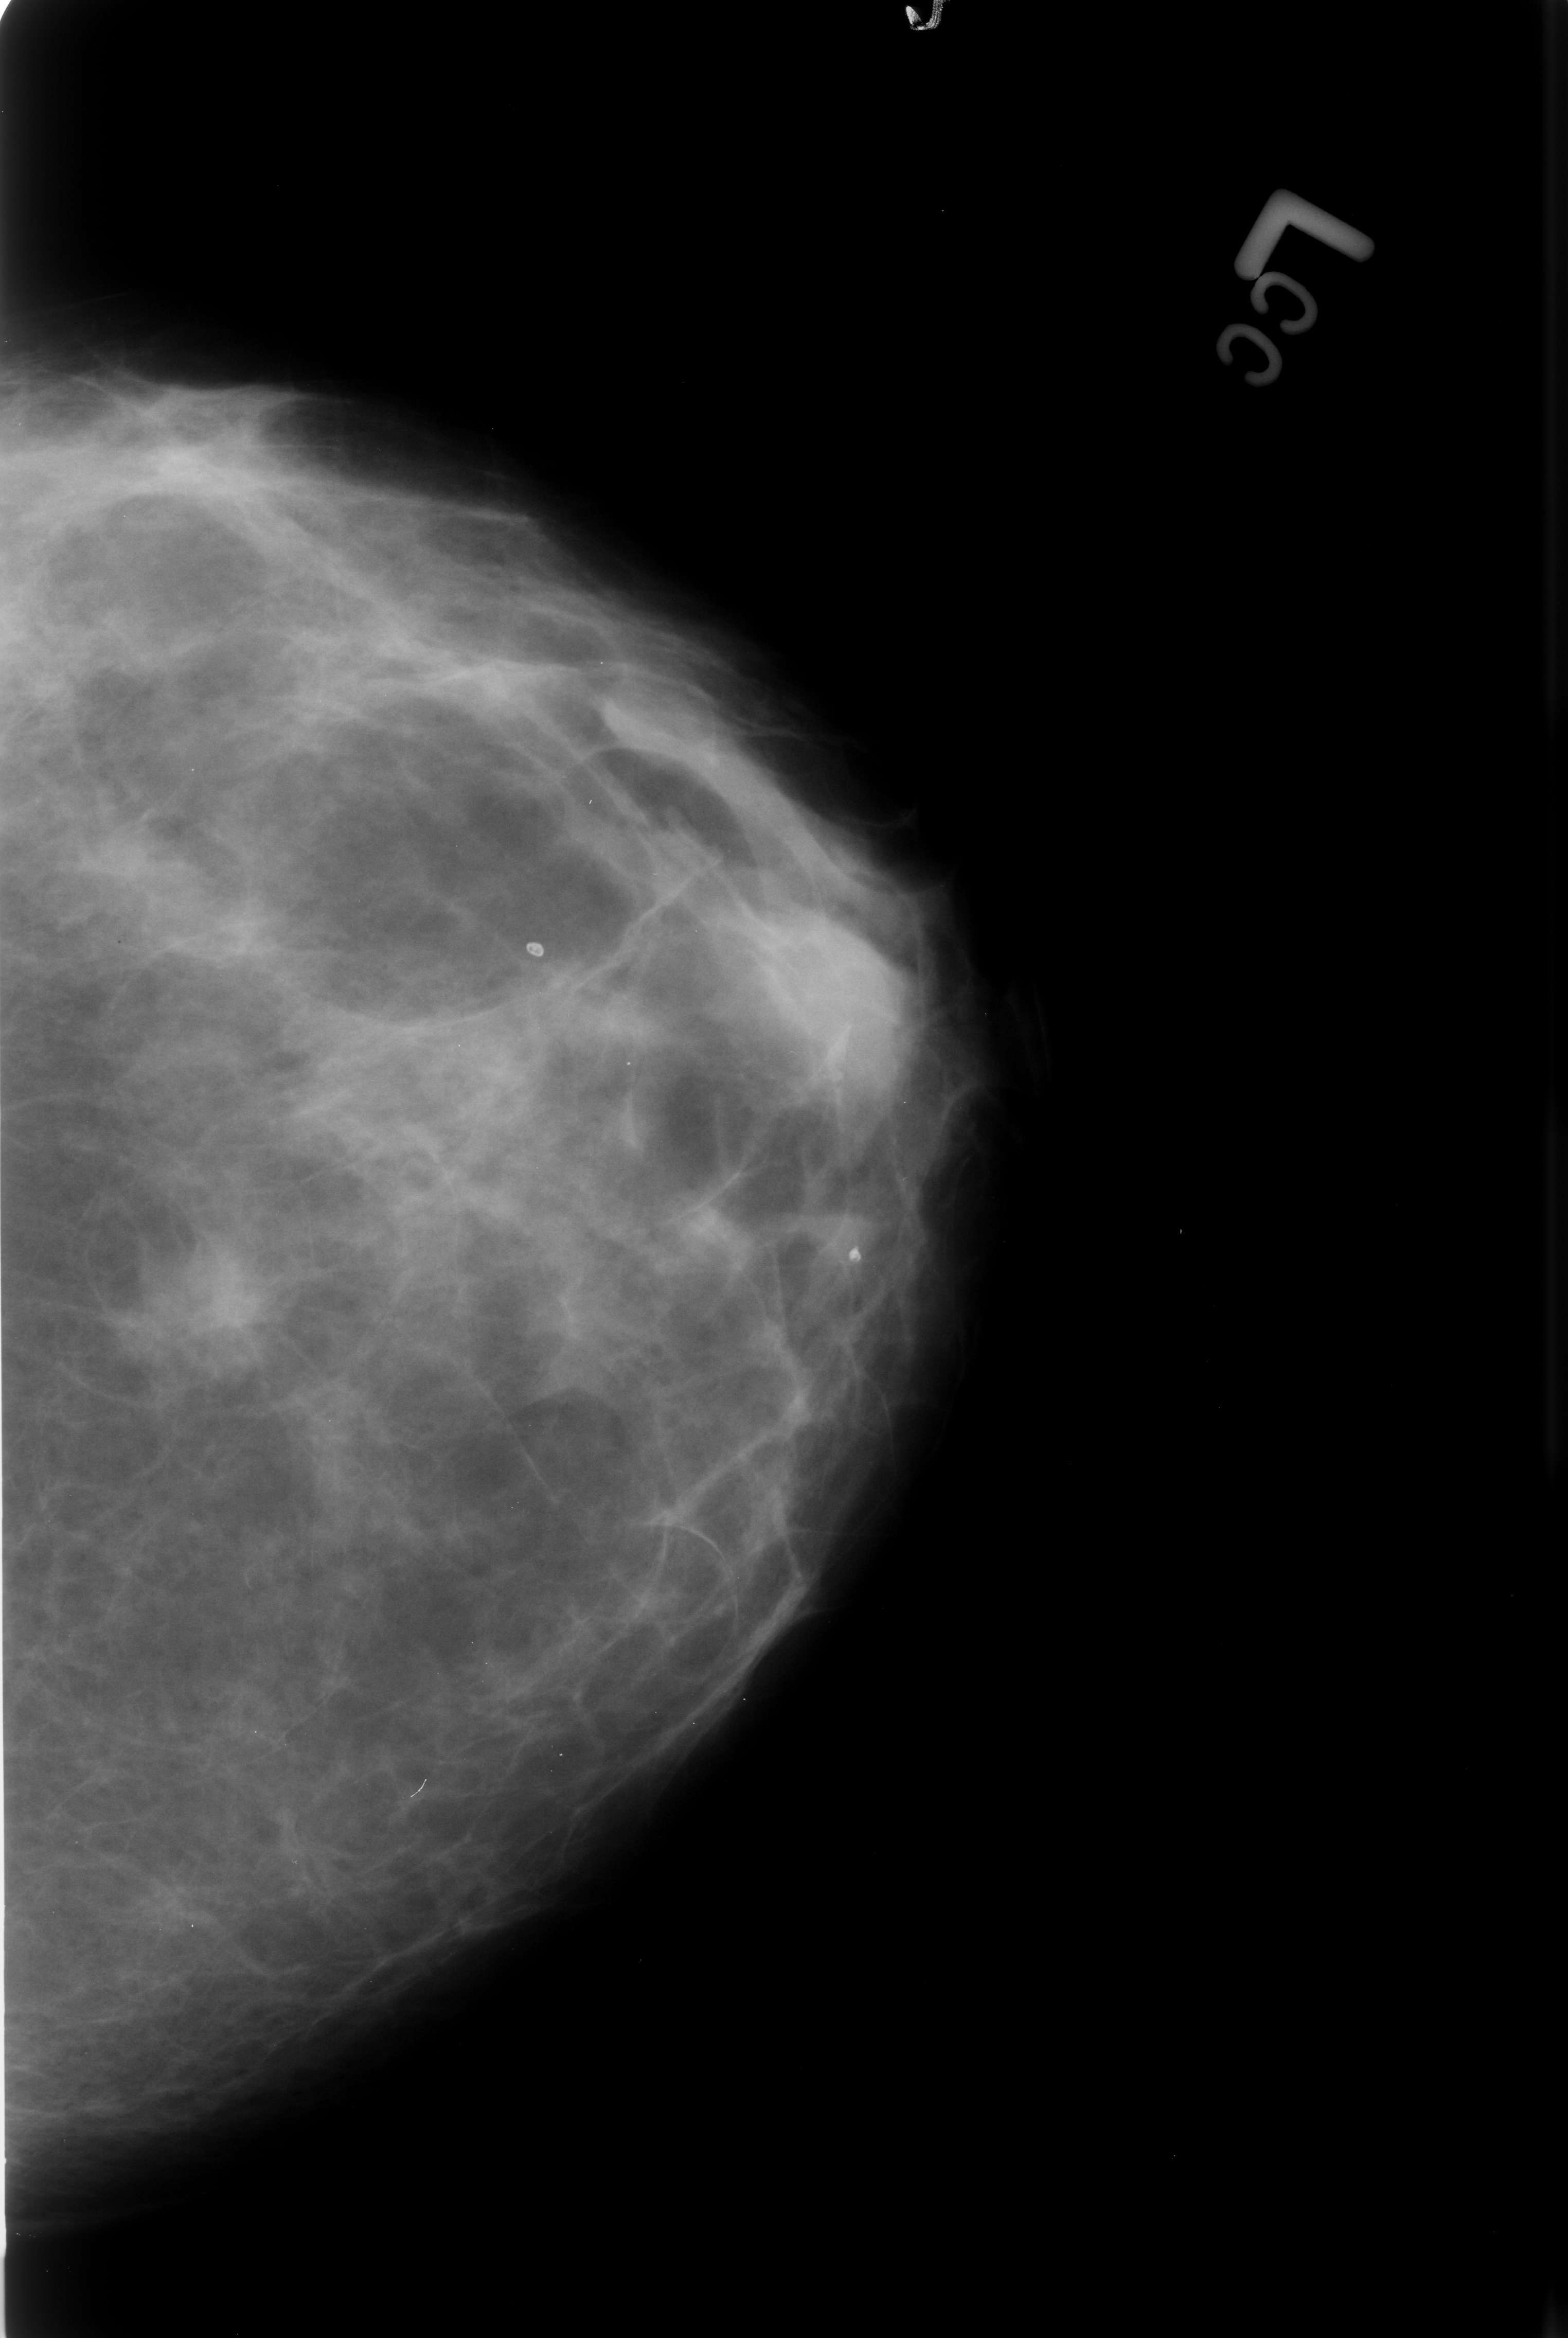
Scanned film-screen mammogram; left breast; craniocaudal (CC) view; breast composition: scattered fibroglandular densities (BI-RADS density category 2 of 4); 1568 × 2338 image matrix.
Marked abnormalities (boxes around the expert regions of interest):
- mass, shape irregular, margins ill defined / spiculated; BI-RADS assessment category 4; subtlety rating 3 on a 1 (subtle) to 5 (obvious) scale; pathology (as recorded): malignant: bounding box [x1, y1, x2, y2] px = [97, 1247, 271, 1386]